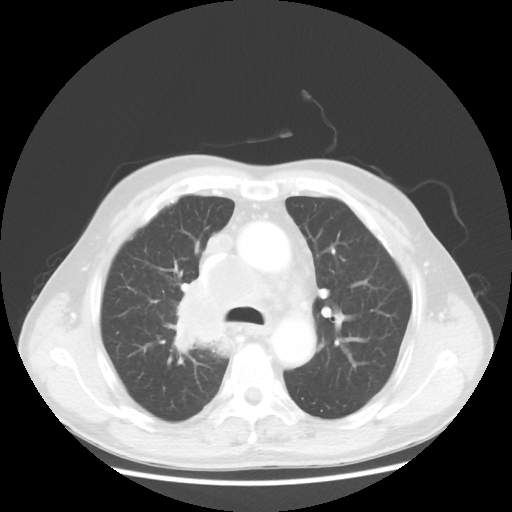
Chest CT, one axial slice. Slice 81 of 124 in the series (ordered by position). 100 kVp. Lung window (W 1500 / L -600 HU). 512 × 512 image matrix, field of view 382 × 382 mm. Patient: male, 64 years. Case-level facts recorded for this patient, not image findings: clinical TNM (as recorded): T3 N3 M0; histopathological grade: G3.
Annotated regions visible in this slice (rectangle marked by the reading radiologist):
- lung tumour (recorded histology: small cell carcinoma): bounding box <164,286,239,368> (left, top, right, bottom; pixels)